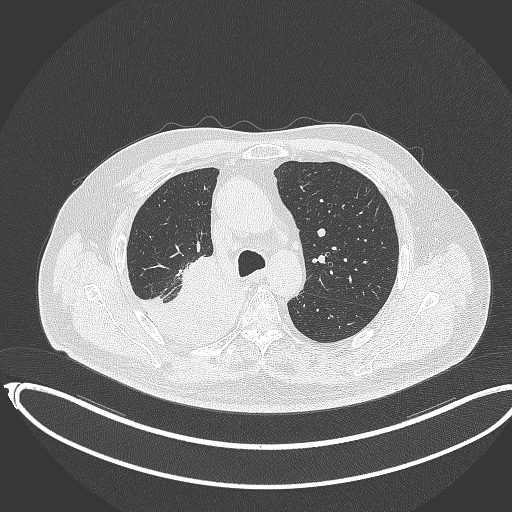
Chest CT, one axial slice; slice 250 of 403 in the series (ordered by position); reconstruction kernel B70f; lung window (W 1500 / L -600 HU); 512 × 512 image matrix, field of view 436 × 436 mm. Patient: male, 68 years. From the clinical record (not read from this slice): clinical TNM (as recorded): T2a N0 M0.
Annotated regions visible in this slice (bounding box drawn by a radiologist):
- lung tumour (recorded histology: adenocarcinoma): bounding box [x1, y1, x2, y2] px = [131, 256, 248, 354]